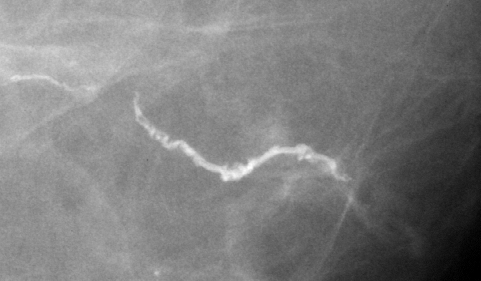
Region of interest cut from a scanned film mammogram (one marked finding), left breast, CC view, BI-RADS breast density category 1 (scale 1–4).
- Finding: calcifications, morphology vascular; BI-RADS assessment category 2; benign; no additional work-up was recommended (benign without callback).